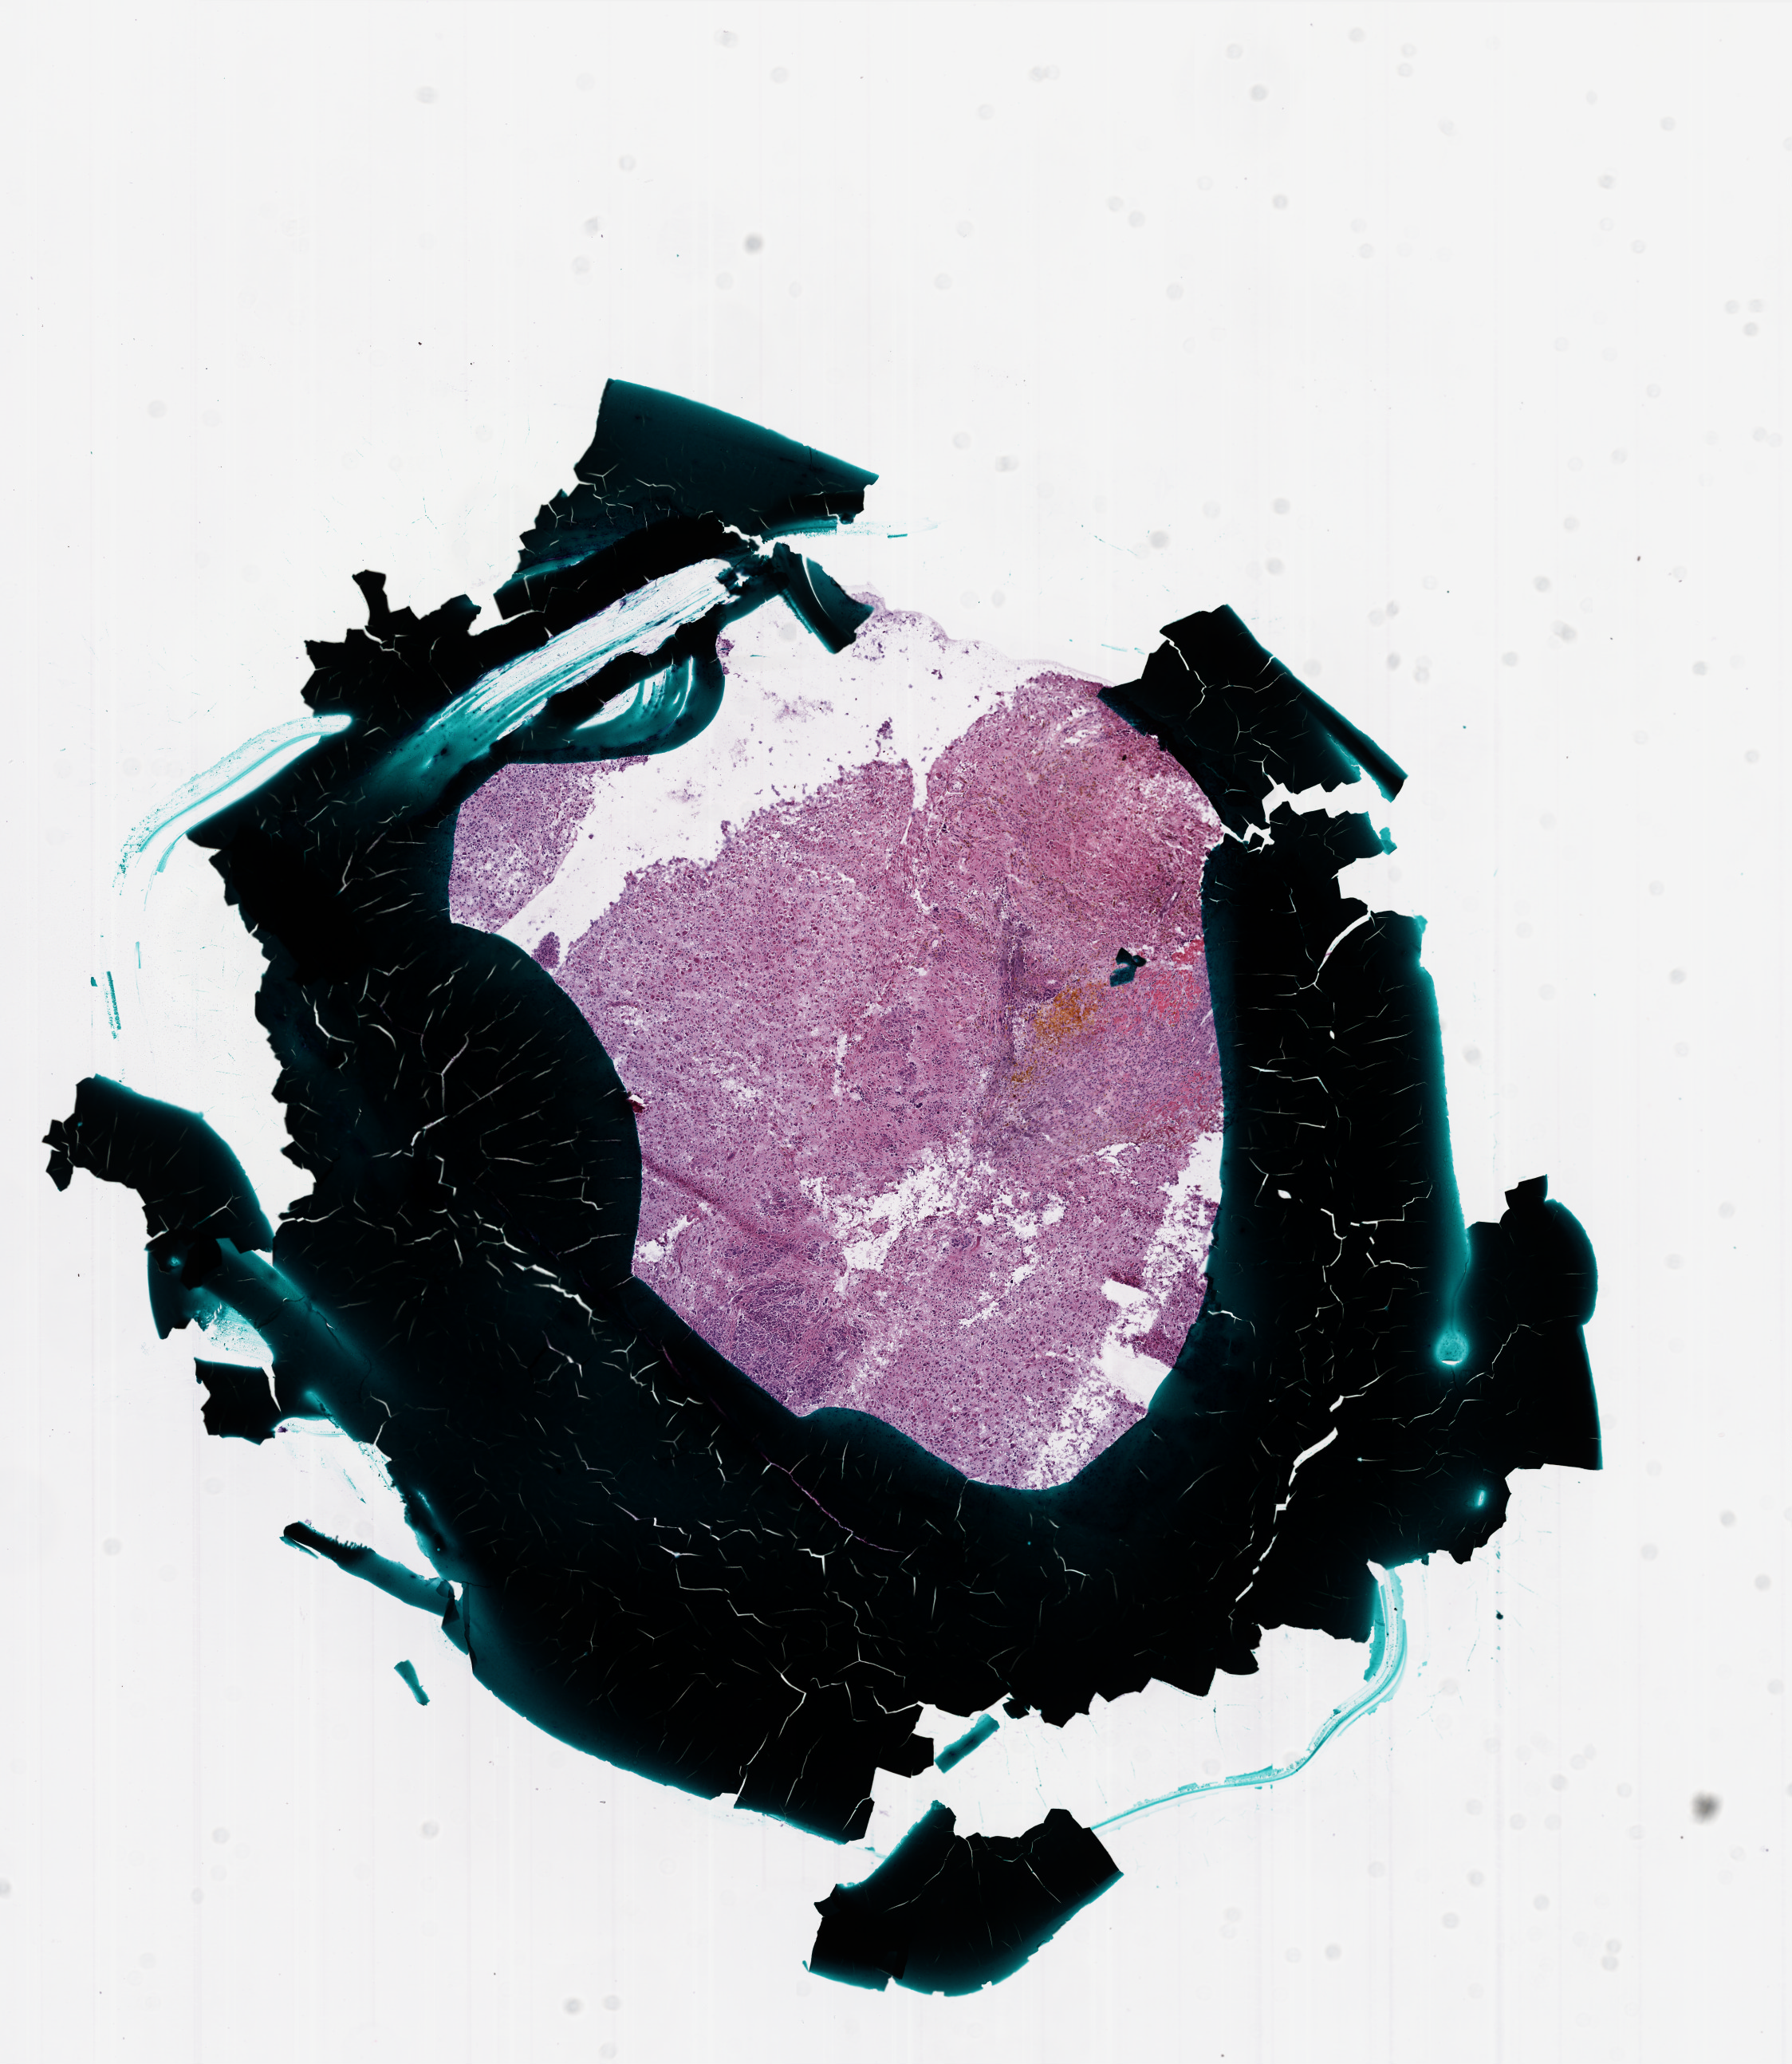
Whole-slide histology image, H&E-stained, low-resolution overview of the scanned area, about 9.0 x 10.4 mm (acquisition: 20x scan); frozen section; sample: primary tumour, brain. Patient: male, age at initial diagnosis 46 years. Pathologist review of this section (percent, as recorded): tumour cells 95%, tumour nuclei 100%, normal cells 0%, stromal cells 0%, necrosis 5%.
• histologic diagnosis: Glioblastoma